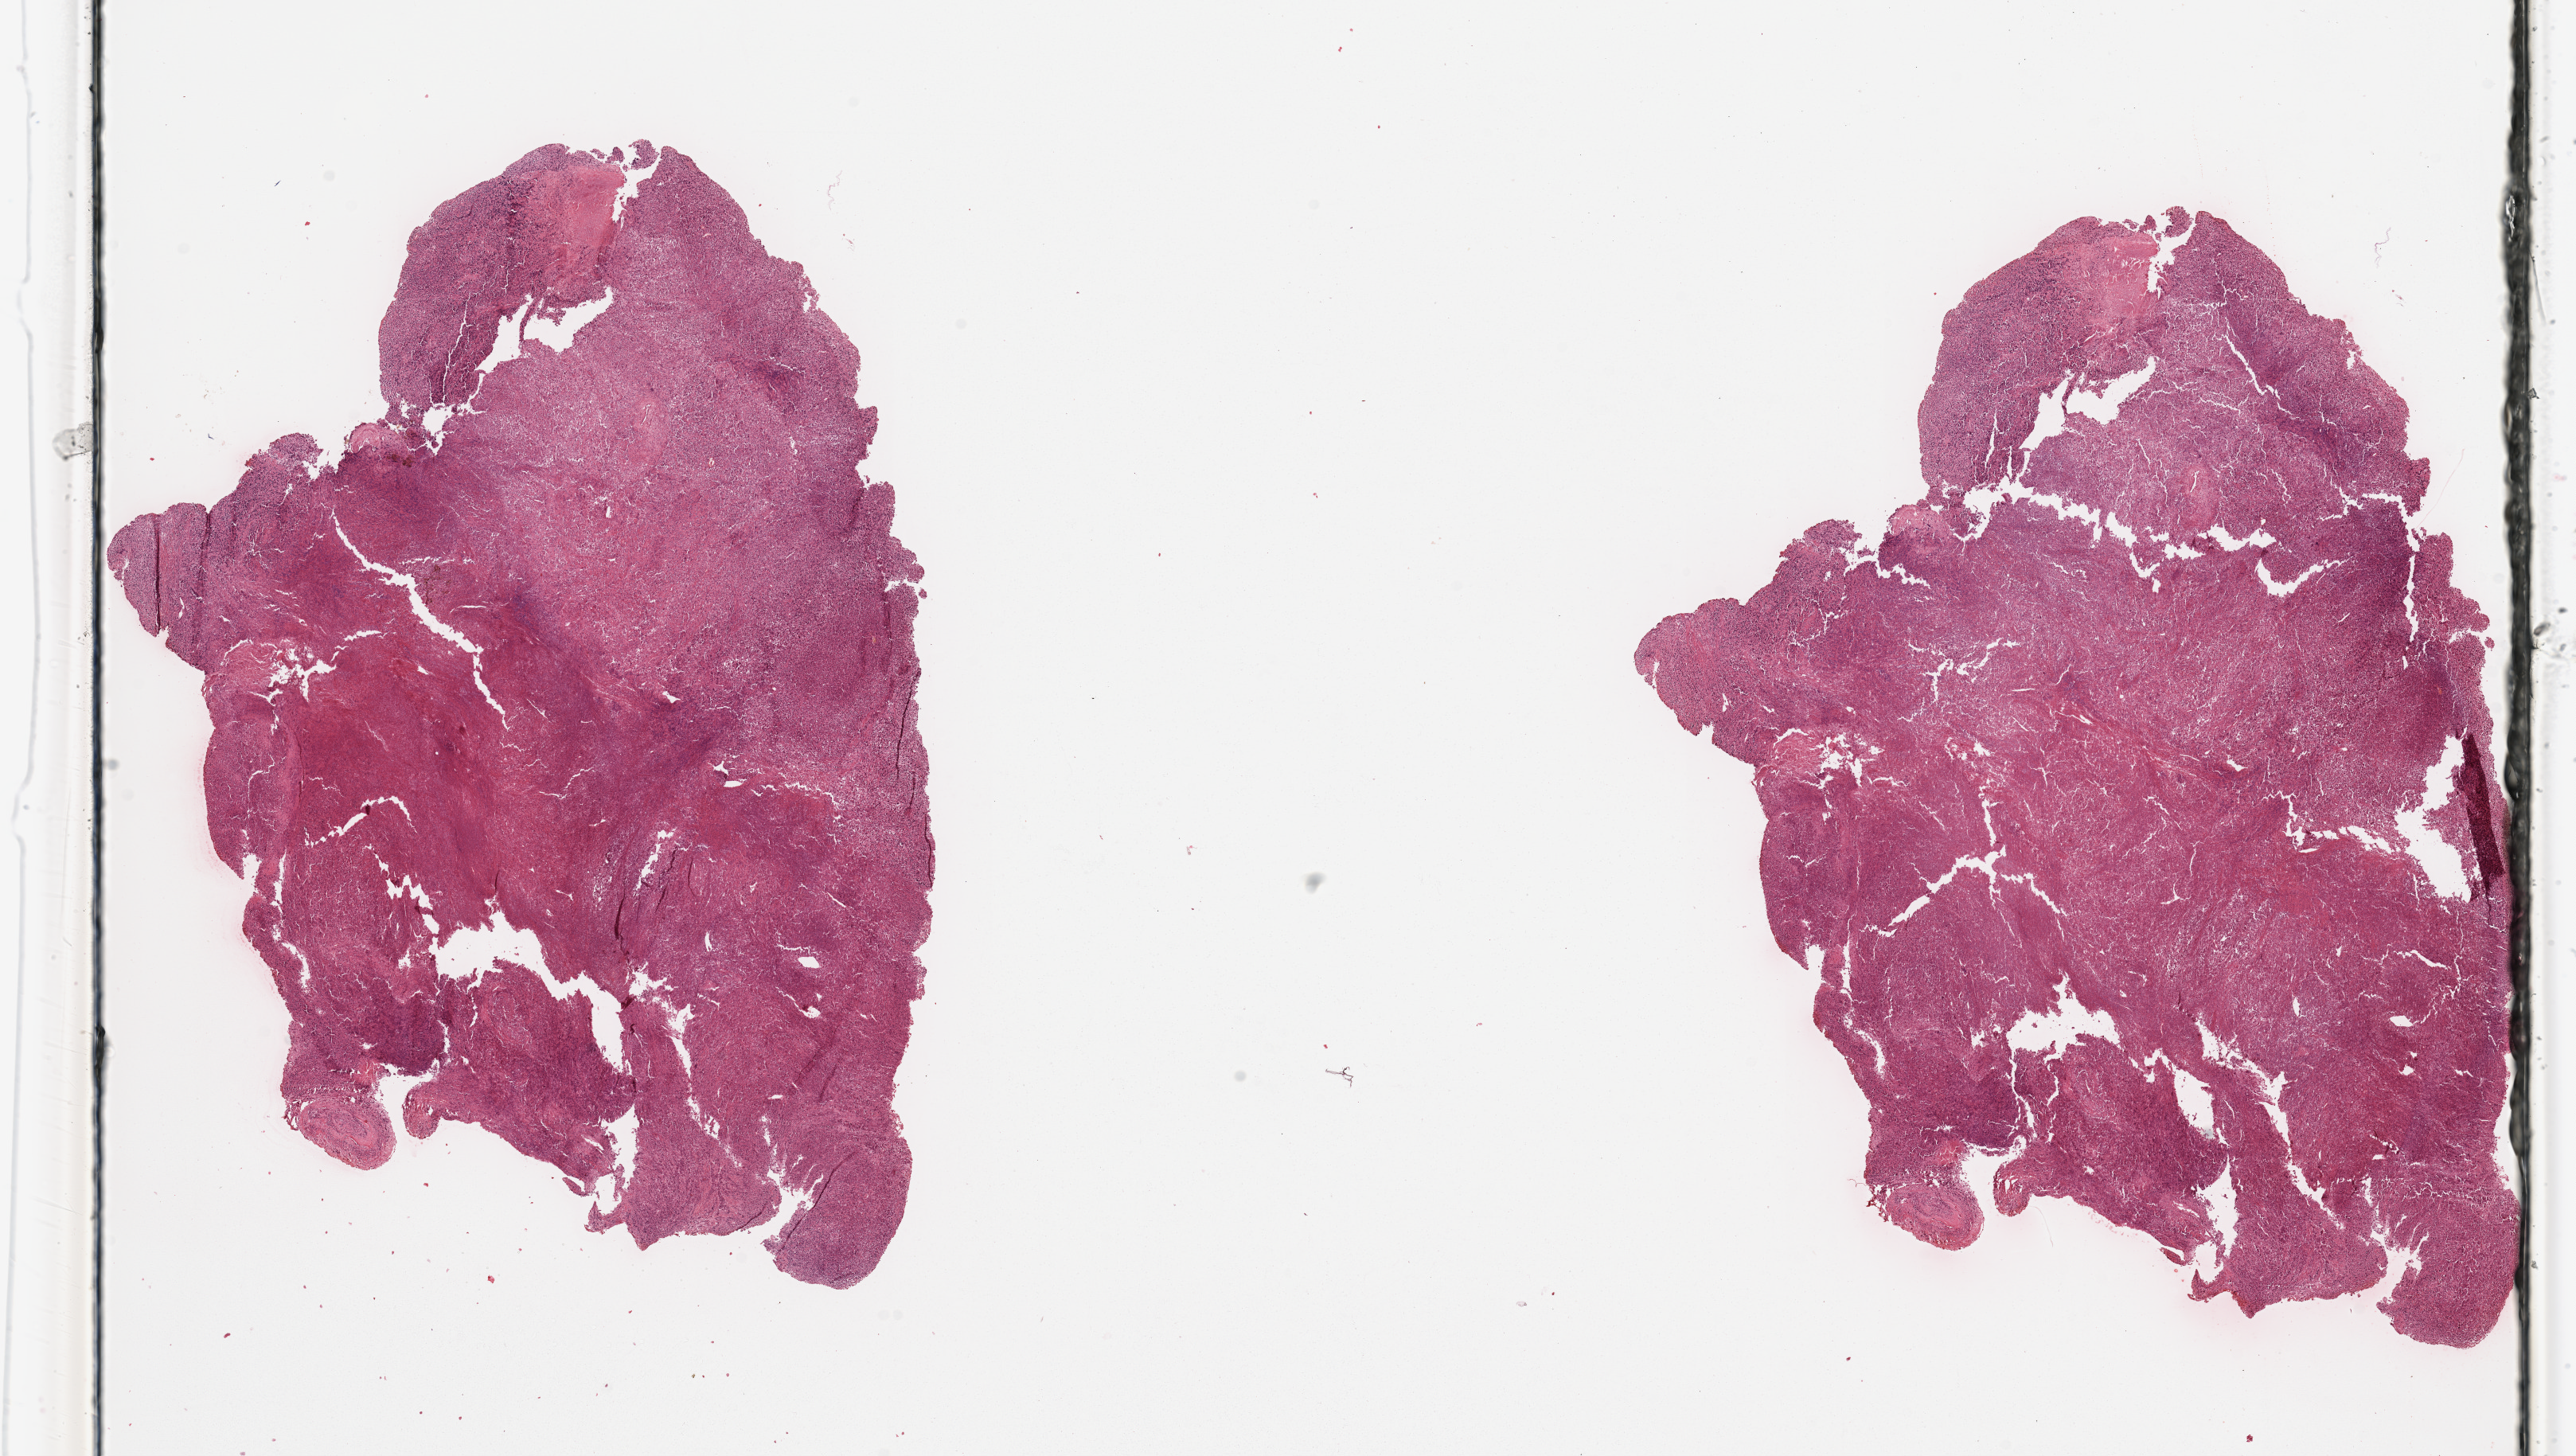
Digitized H&E tissue section (whole slide), whole scanned area (about 25.6 x 14.5 mm, acquisition: 20x scan) shown as a low-resolution overview. 80-year-old female patient.
Patient diagnosis (cohort enrolment): sarcoma (site not recorded at cohort level). Primary tumour site (as recorded): gynecologic.